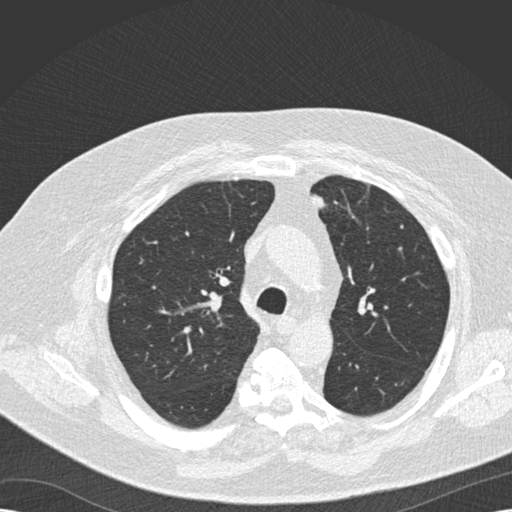
Low-dose screening chest CT, one axial slice; position 117 of 173 along the scan axis; reconstruction kernel B30f; 120 kVp; lung window (W 1500 / L -600 HU); 2 mm slice thickness; 512 × 512 image matrix, field of view 370 × 370 mm.
Structures marked on this image (outlined manually by an expert reader):
- lesion 1 (tumor, upper lobe of left lung): box from (x=312, y=194) to (x=324, y=207) px